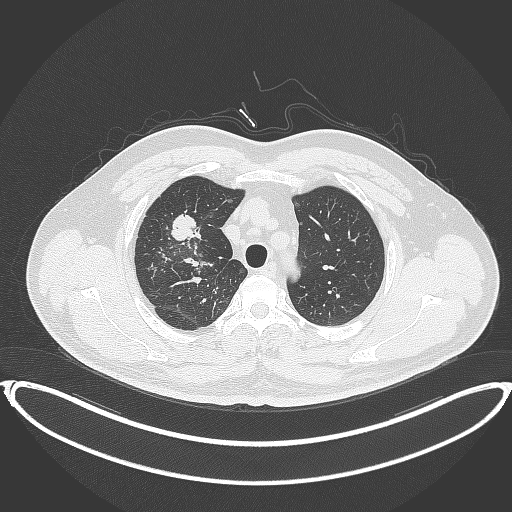
Chest CT, one axial slice. Slice 305 of 399 in the series (ordered by position). 120 kVp. Lung window (W 1500 / L -600 HU). 512 × 512 image matrix, field of view 445 × 445 mm. Patient: male, 53 years. From the clinical record (not read from this slice): clinical TNM (as recorded): T2a N0 M0.
Outlined on this slice (bounding box drawn by a radiologist):
- lung tumour (recorded histology: adenocarcinoma): bounding box [x1, y1, x2, y2] px = [168, 211, 200, 245]